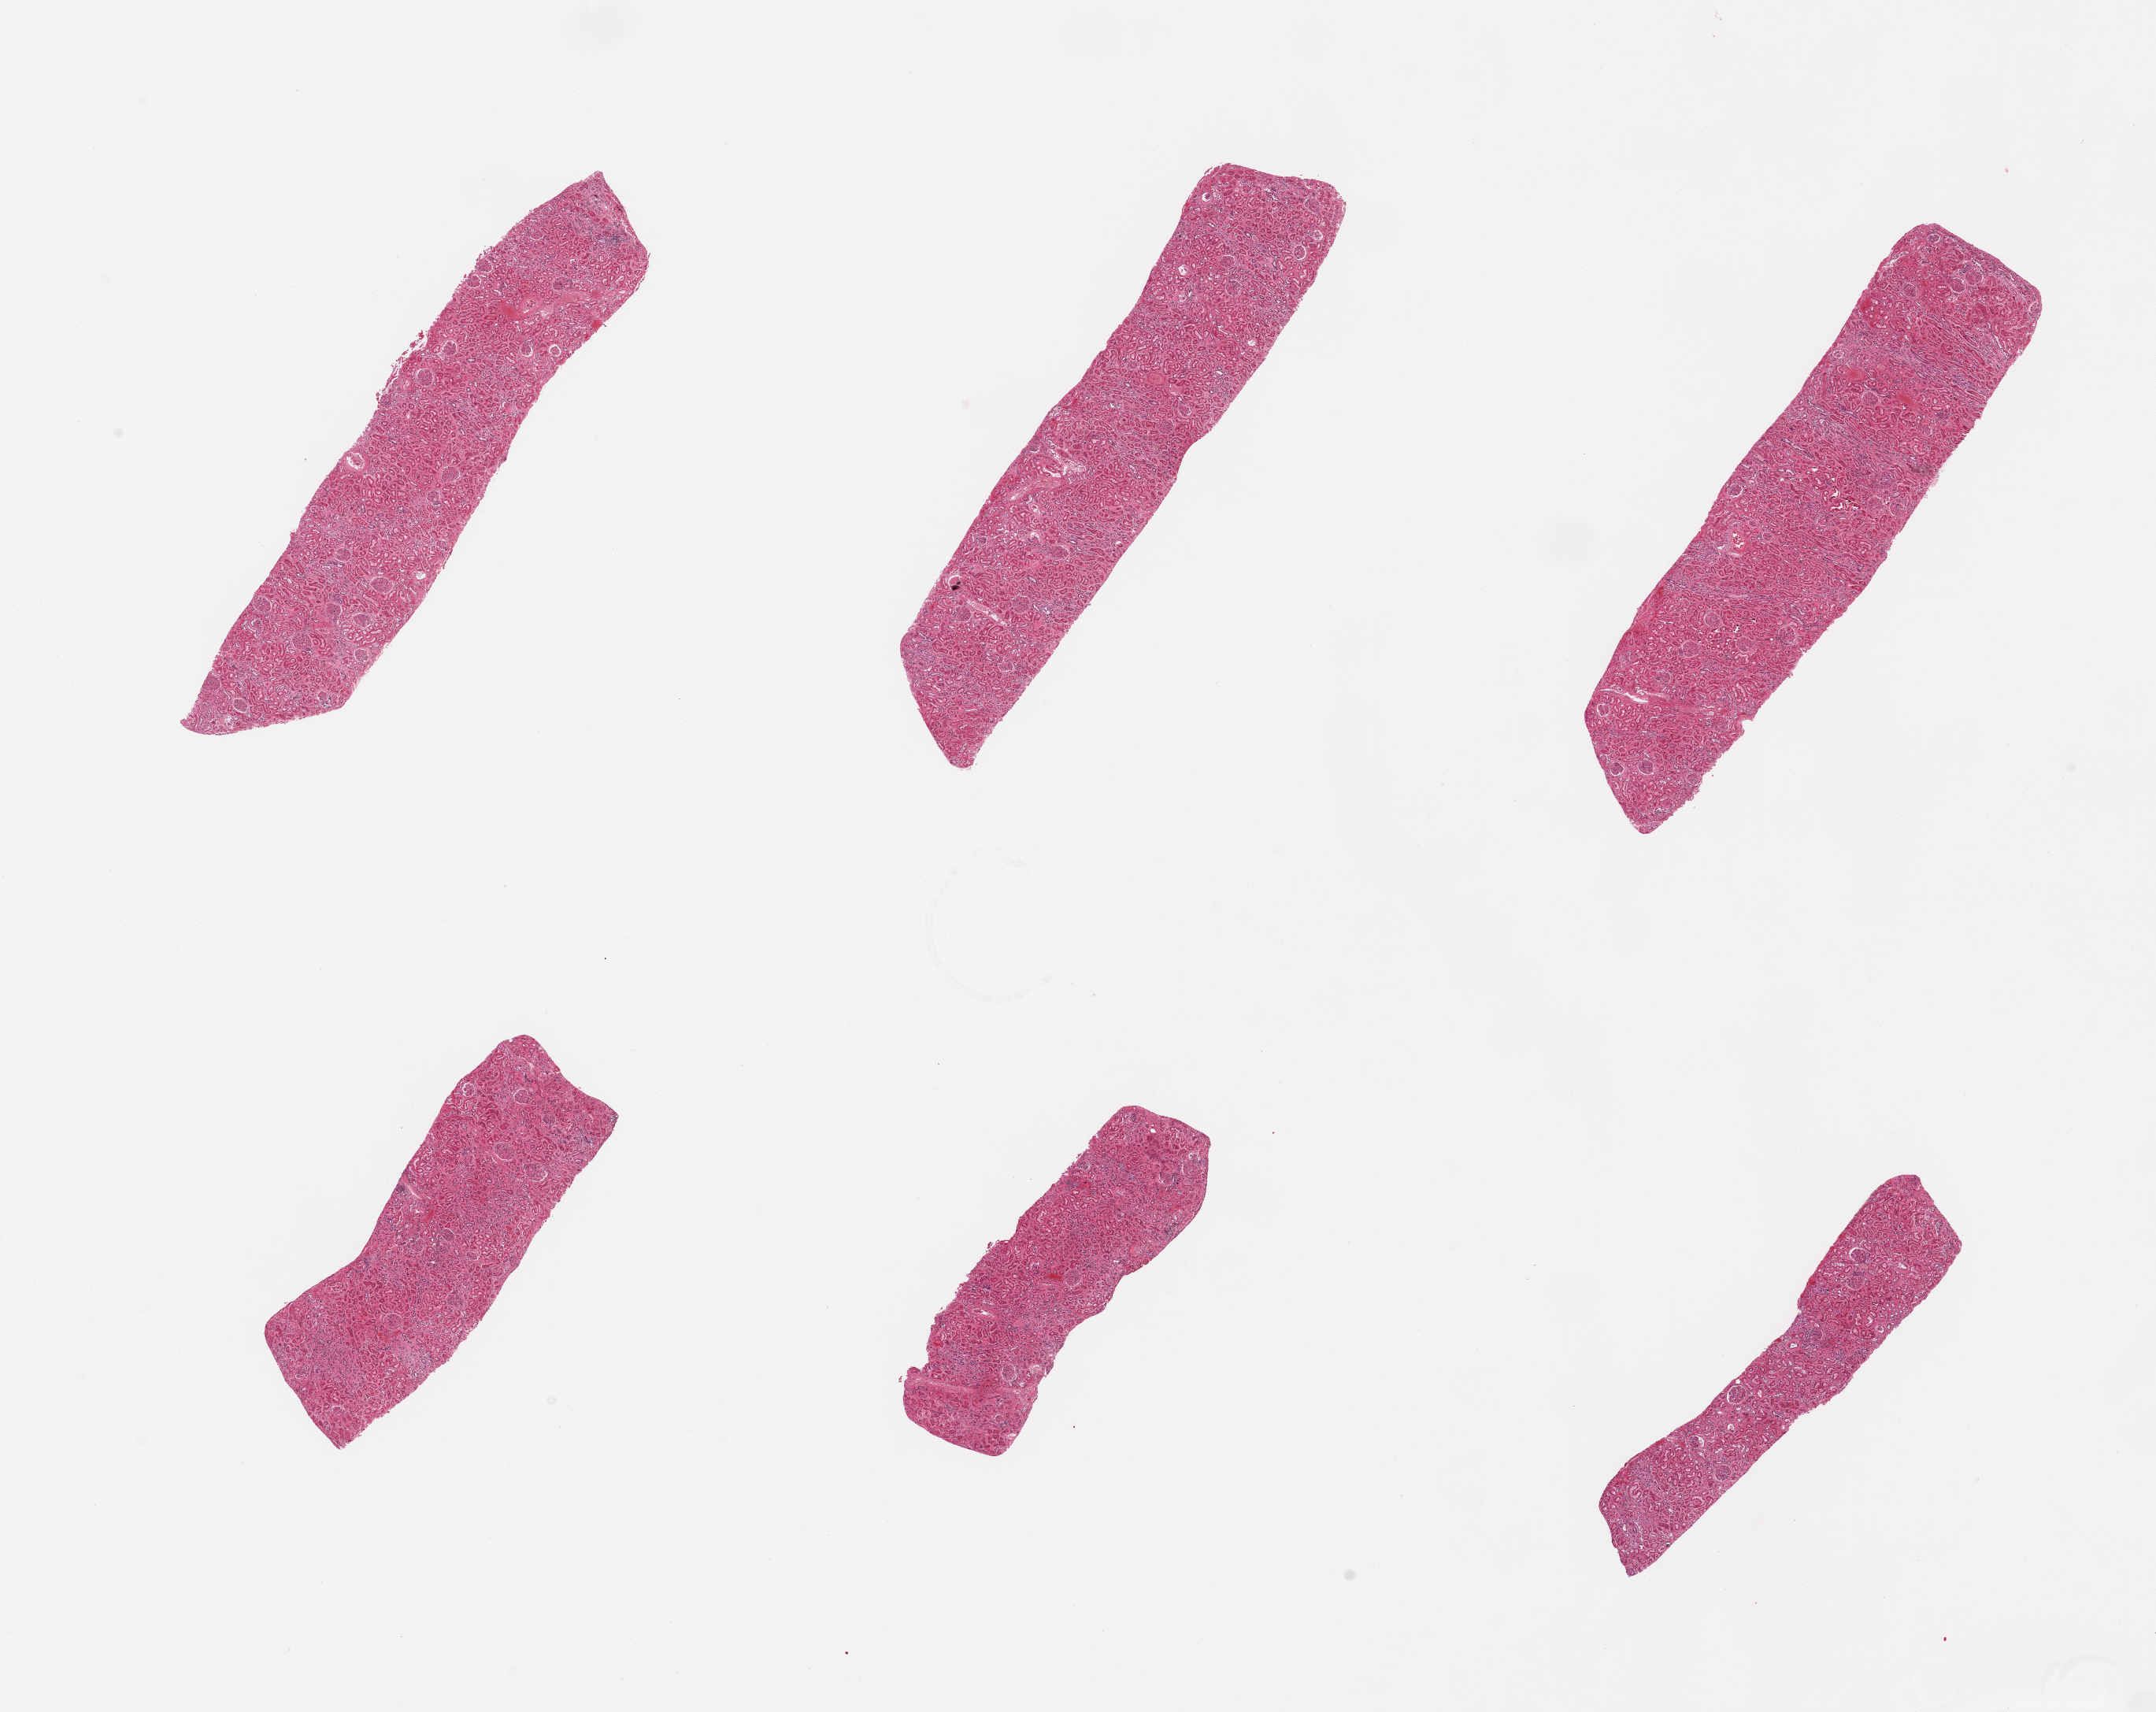
H&E whole-slide image — shown as a low-resolution overview of the whole scanned area (about 21.7 x 17.2 mm, from a 20x scan); PAXgene-fixed paraffin-embedded (PFPE) section; target tissue: renal cortex; tissue donor sample. Female donor.
• reviewer comment on this tissue sample: 6 pieces; no active or chronic lesions; tubules autolyzed